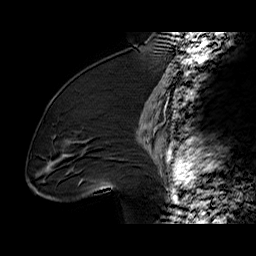
Breast MRI (dynamic contrast-enhanced), one sagittal slice. Position 35 of 60 along the scan axis. Dynamic contrast-enhanced series, time point 2 of 6 at this slice position (early post-contrast). 1.5 T. TE 6.2 ms, TR 32.4 ms. 256 × 256 image matrix, field of view 200 × 200 mm. Female patient. Case-level facts recorded for this patient, not image findings: setting: breast cancer imaged before/during neoadjuvant chemotherapy; receptor status: triple-negative.
Structures marked on this image (semi-automatically segmented with operator editing):
- analysis volume of interest (the breast-tissue region the enhancement analysis was run in; not a lesion): bounding box <36,97,134,196> (left, top, right, bottom; pixels)
- tumour enhancement mask (voxels above the 100 % enhancement threshold inside the analysis volume of interest): <67,156,105,185>